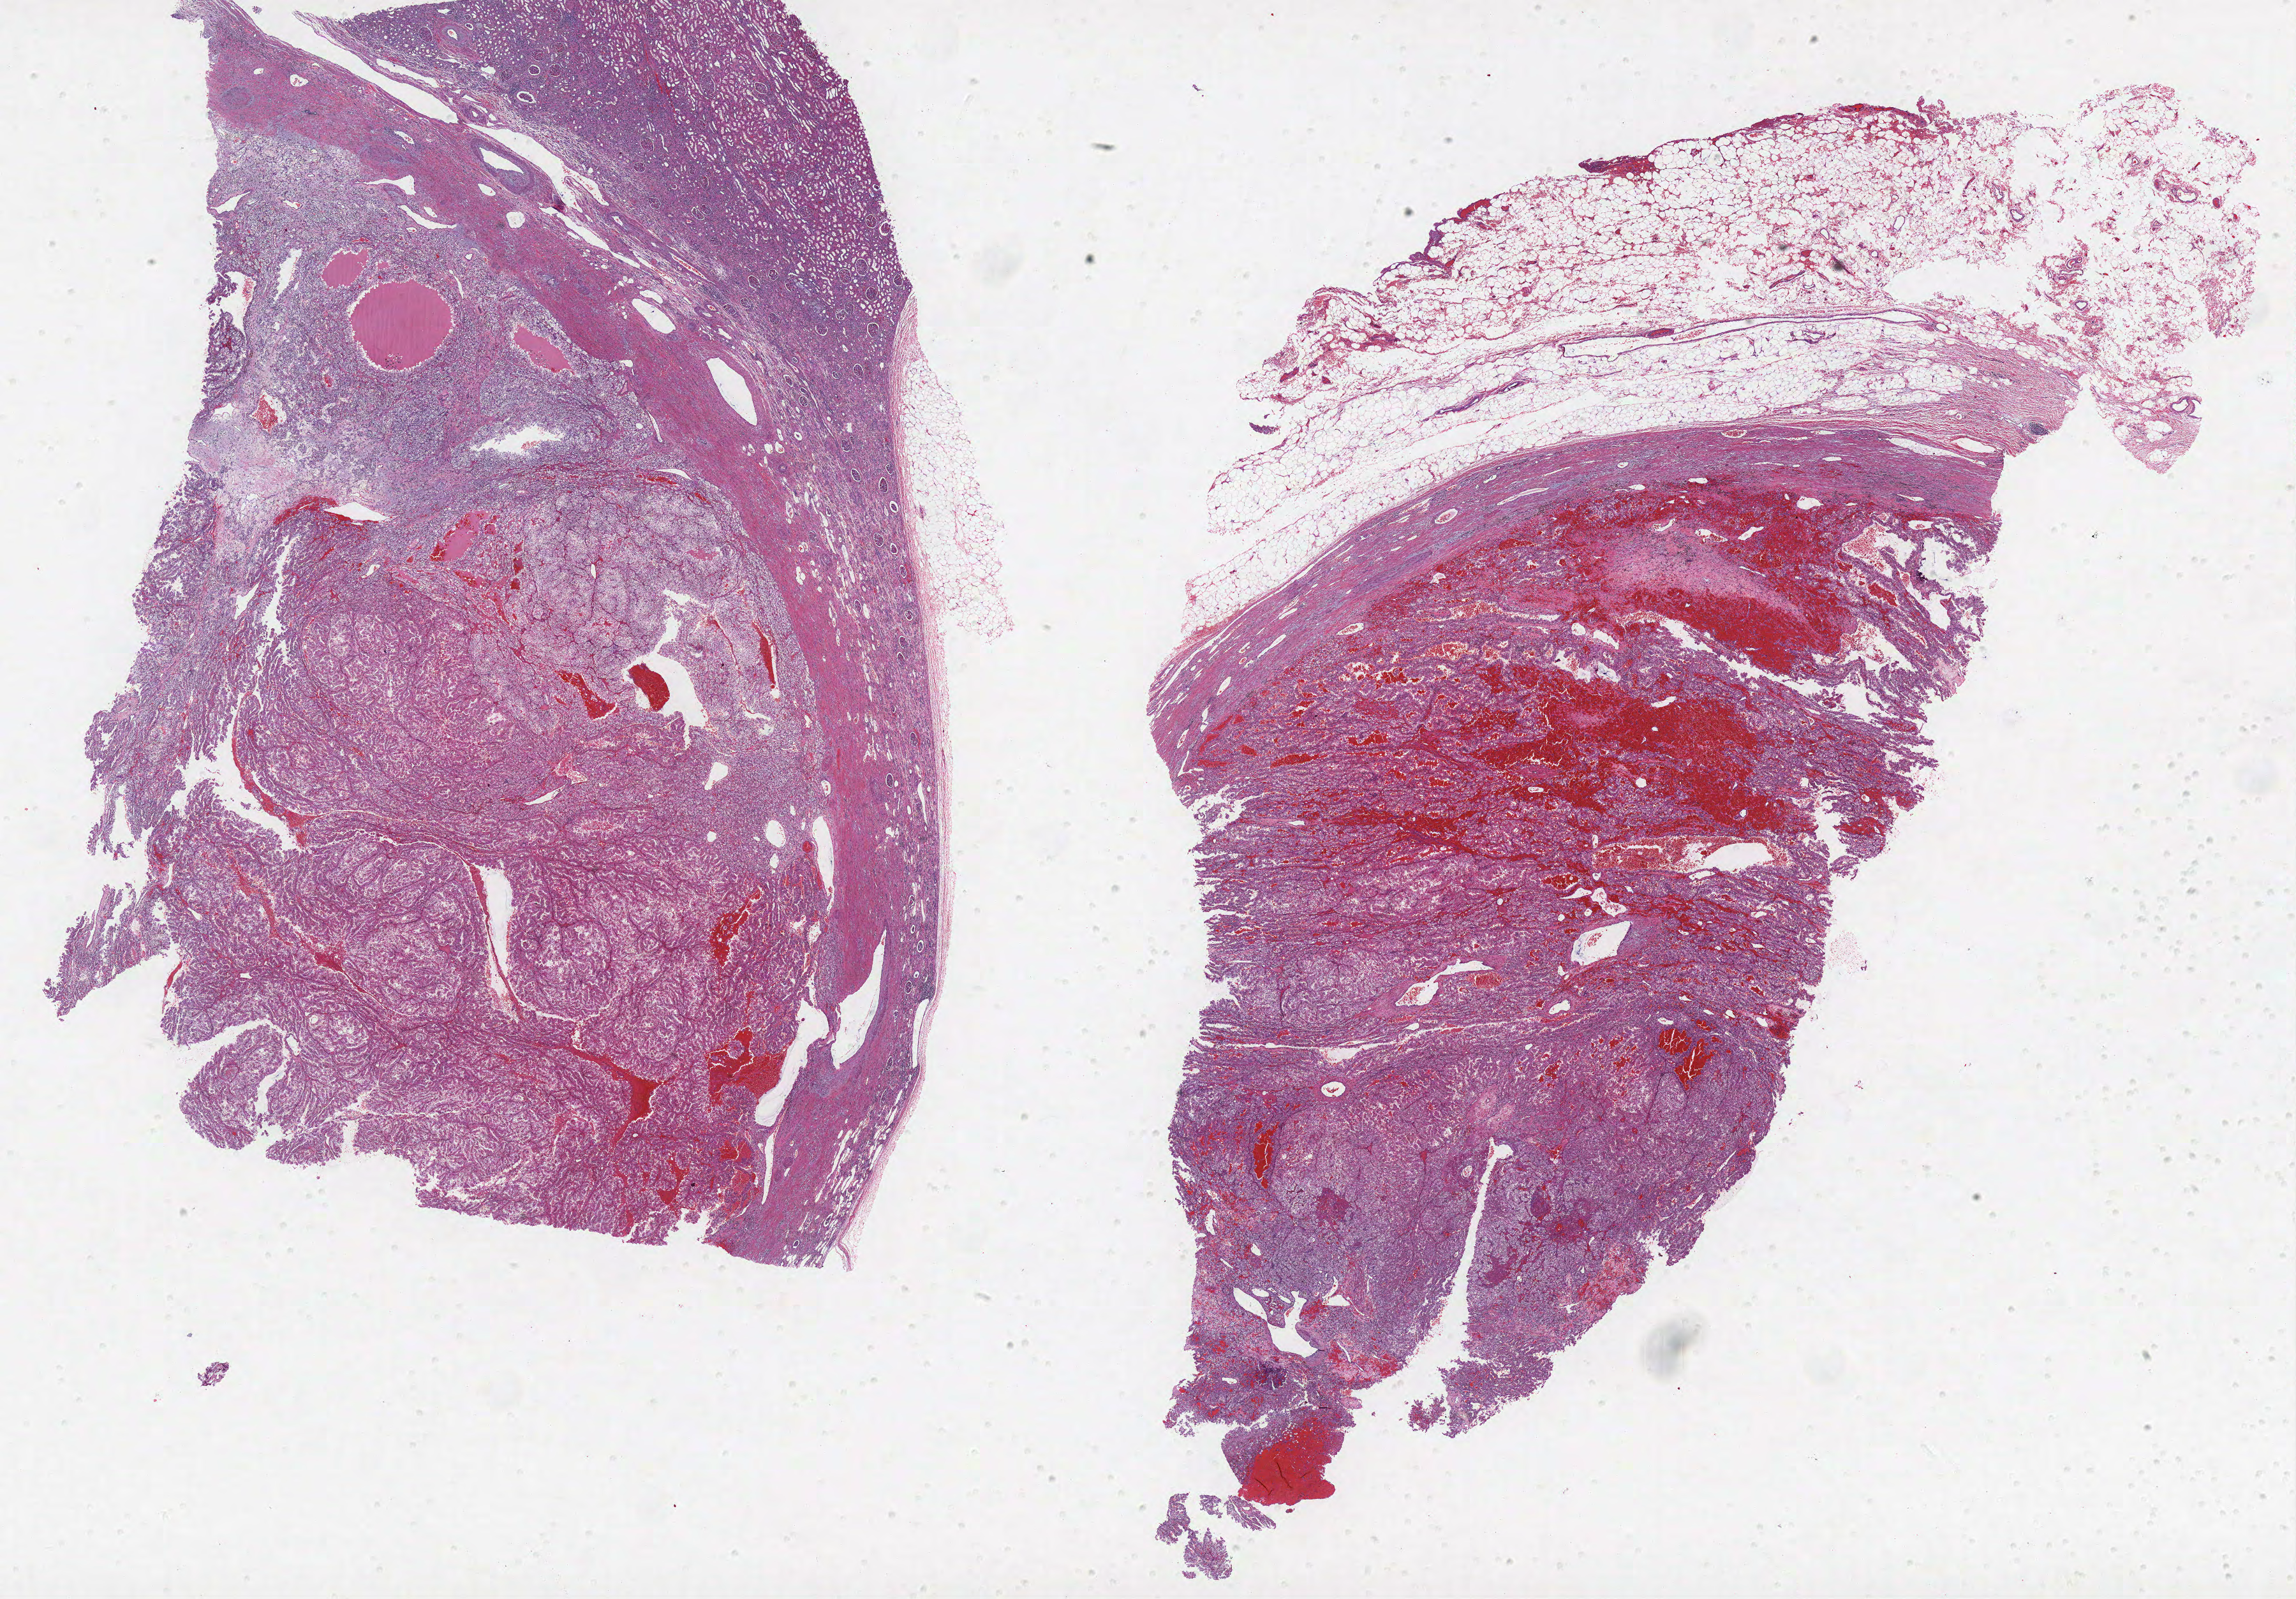
Whole-slide histology image, H&E, a low-resolution overview of the entire scanned area, about 28.8 x 20.0 mm (from a 40x scan); formalin-fixed paraffin-embedded (FFPE) diagnostic section; primary tumour sample from the kidney. Male patient; age at initial diagnosis 61 years. Histologic grade: G3 (poorly differentiated).
* diagnosis: Clear cell adenocarcinoma, NOS
* AJCC pathologic stage: I